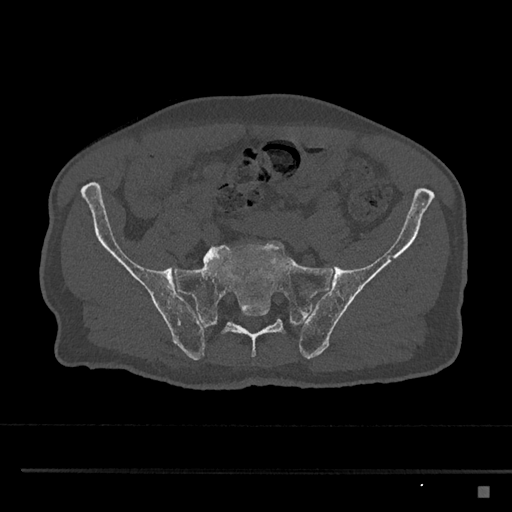
CT including the spine, one axial slice. Position 517 of 797 along the scan axis. Reconstruction kernel Br40s/3. Bone window (W 1800 / L 400 HU). 0.5 mm slice thickness. 512 × 512 image matrix, field of view 391 × 391 mm. Patient: male, 59 years. From the clinical record (not read from this slice): primary cancer: prostate.
Annotated regions visible in this slice (semi-automatic segmentation, software-assisted and operator-edited):
- L5 vertebra: bounding box (x1, y1, x2, y2) in pixels: (203, 253, 210, 260)